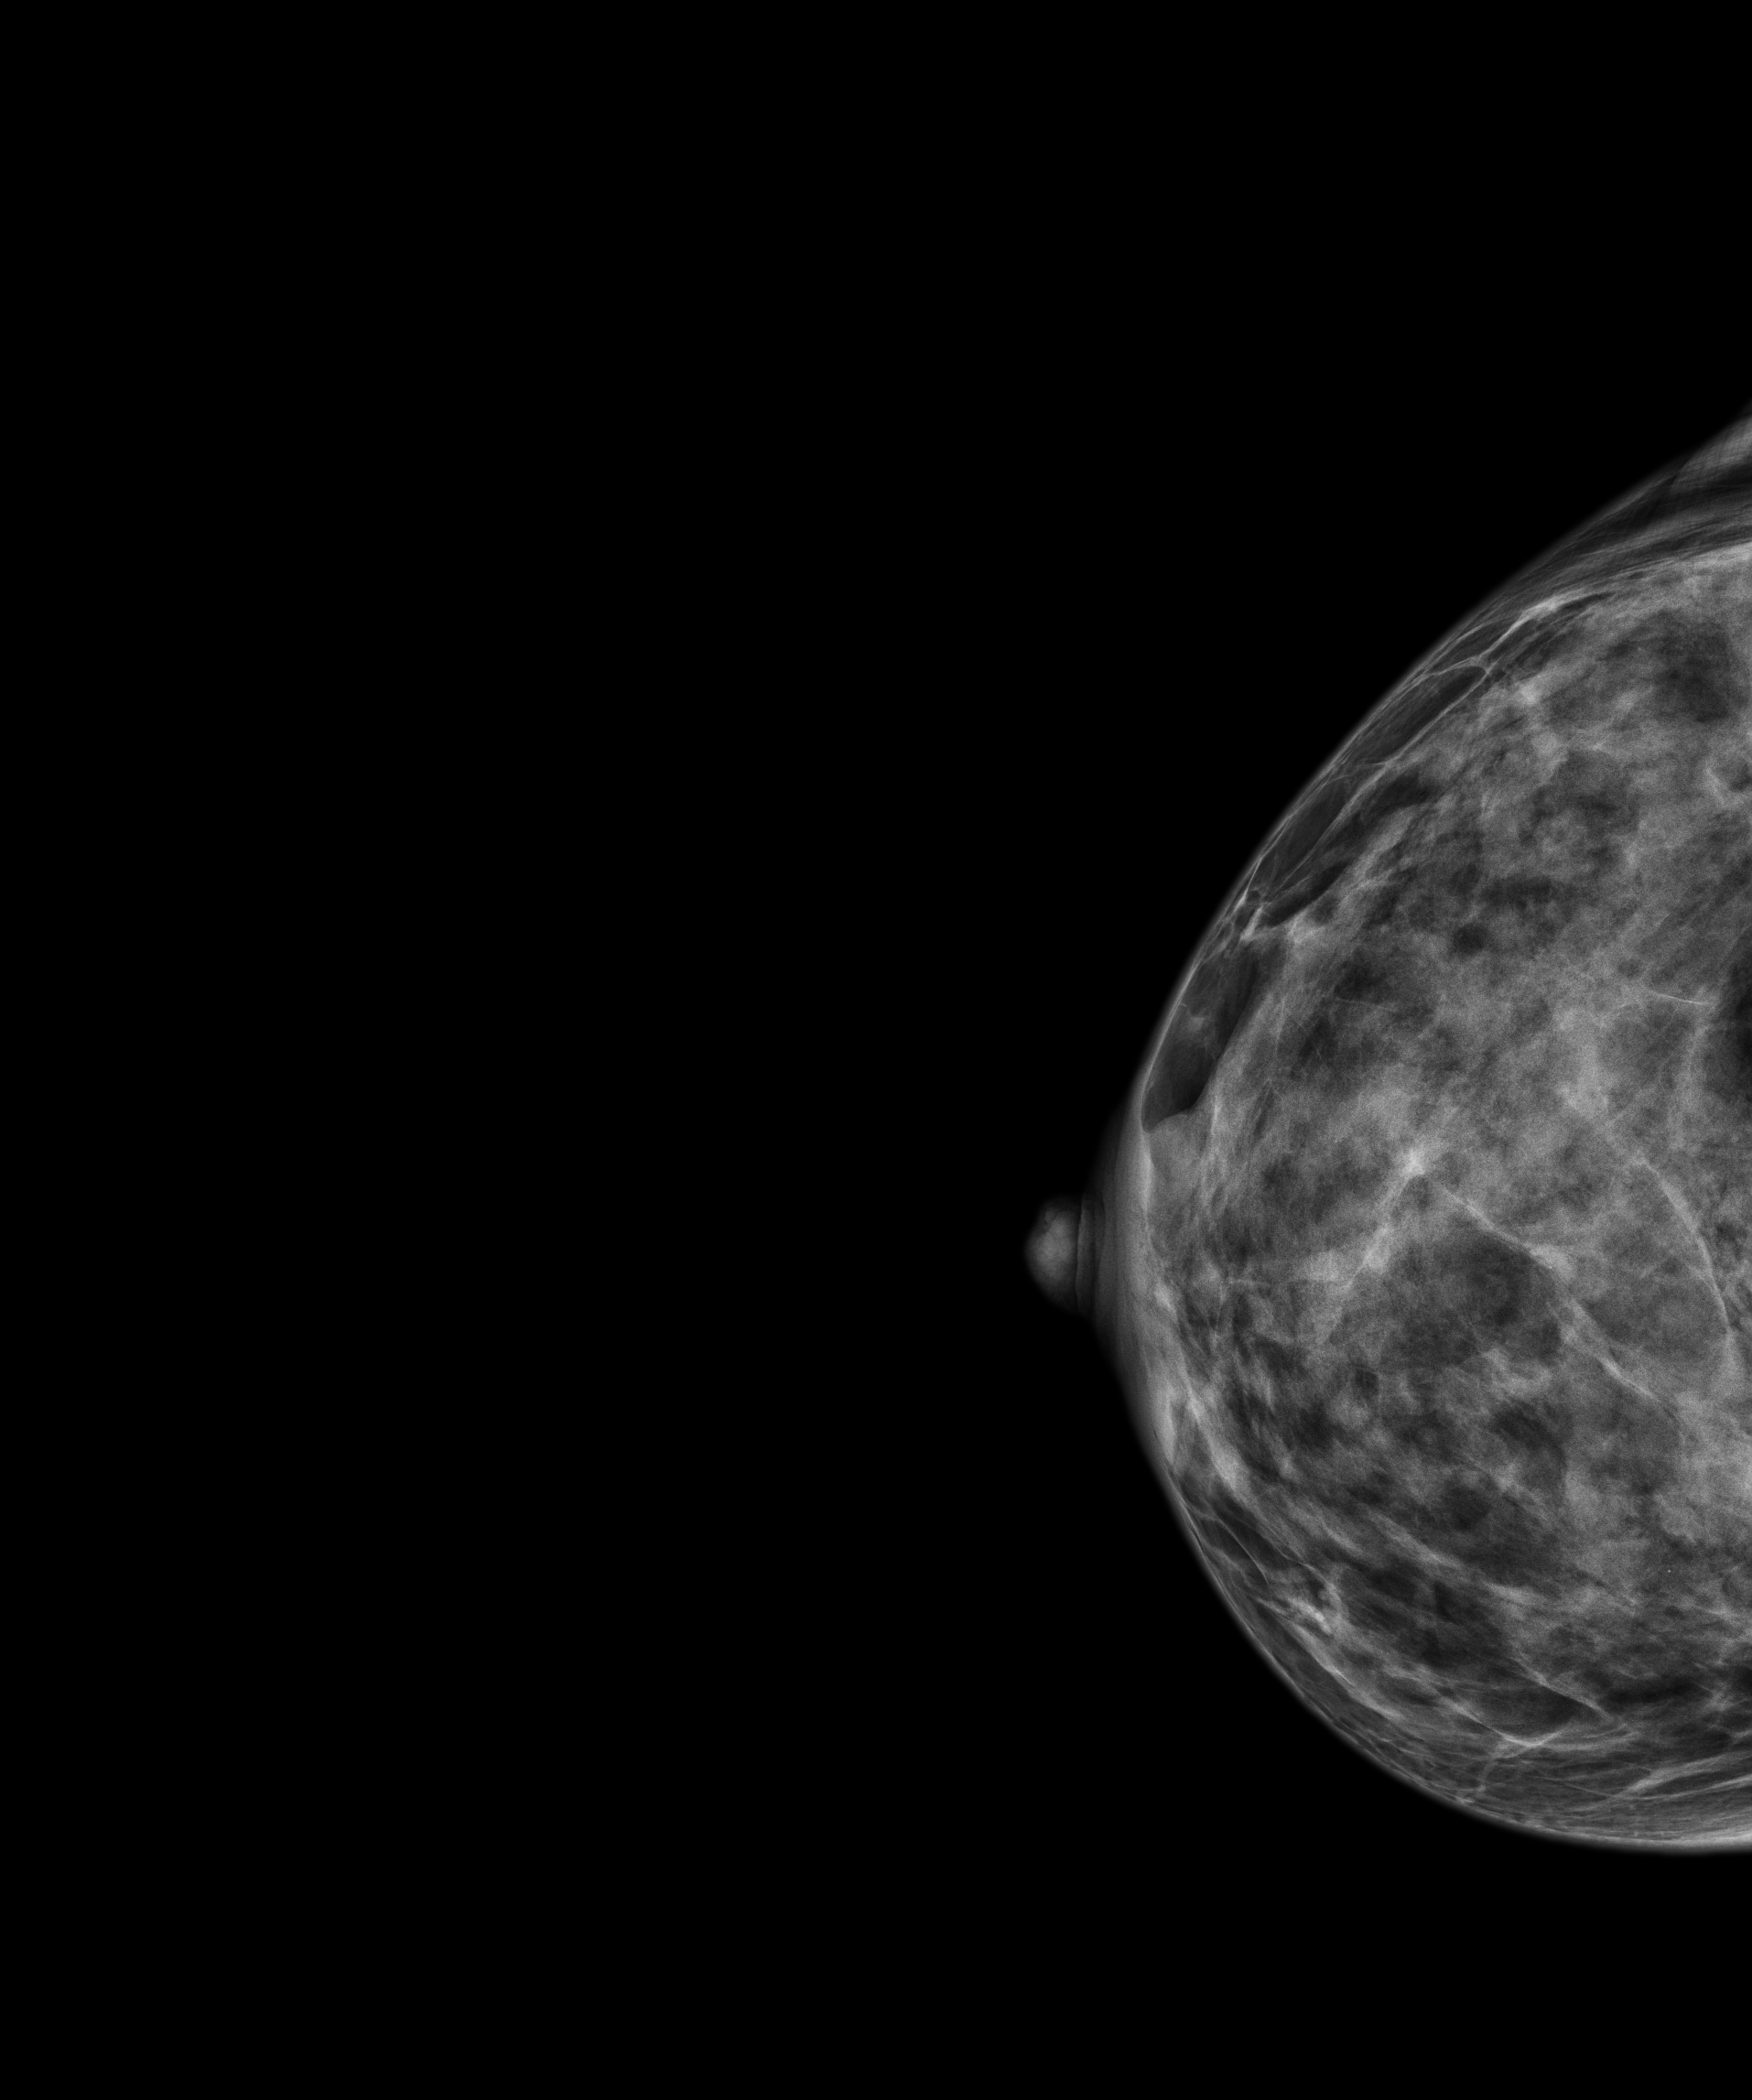
Full-field digital mammogram (FFDM); right breast; craniocaudal (CC) view; screening examination; compressed breast thickness 34 mm. Female patient, age 45 years.
Breast density at the screening exam (both breasts): heterogeneously dense (BI-RADS density category c). Final BI-RADS category for the screening round (tomosynthesis exam, both breasts): category 1. Recall: no recall after this screen.